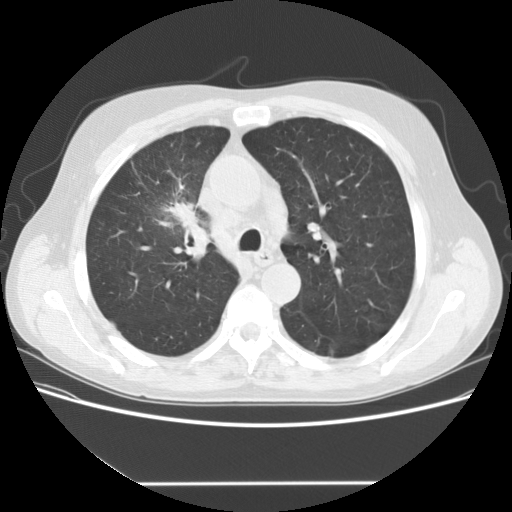
Low-dose screening chest CT, one axial slice. Slice 106 of 153 in the series (ordered by position). Reconstruction kernel STANDARD. Lung window (W 1500 / L -600 HU). 2.5 mm slice thickness. 512 × 512 image matrix, field of view 360 × 360 mm.
Annotated regions visible in this slice (manually delineated by an expert):
- lesion 1 (tumor, upper lobe of right lung): bounding box (x1, y1, x2, y2) in pixels: (164, 201, 200, 229)